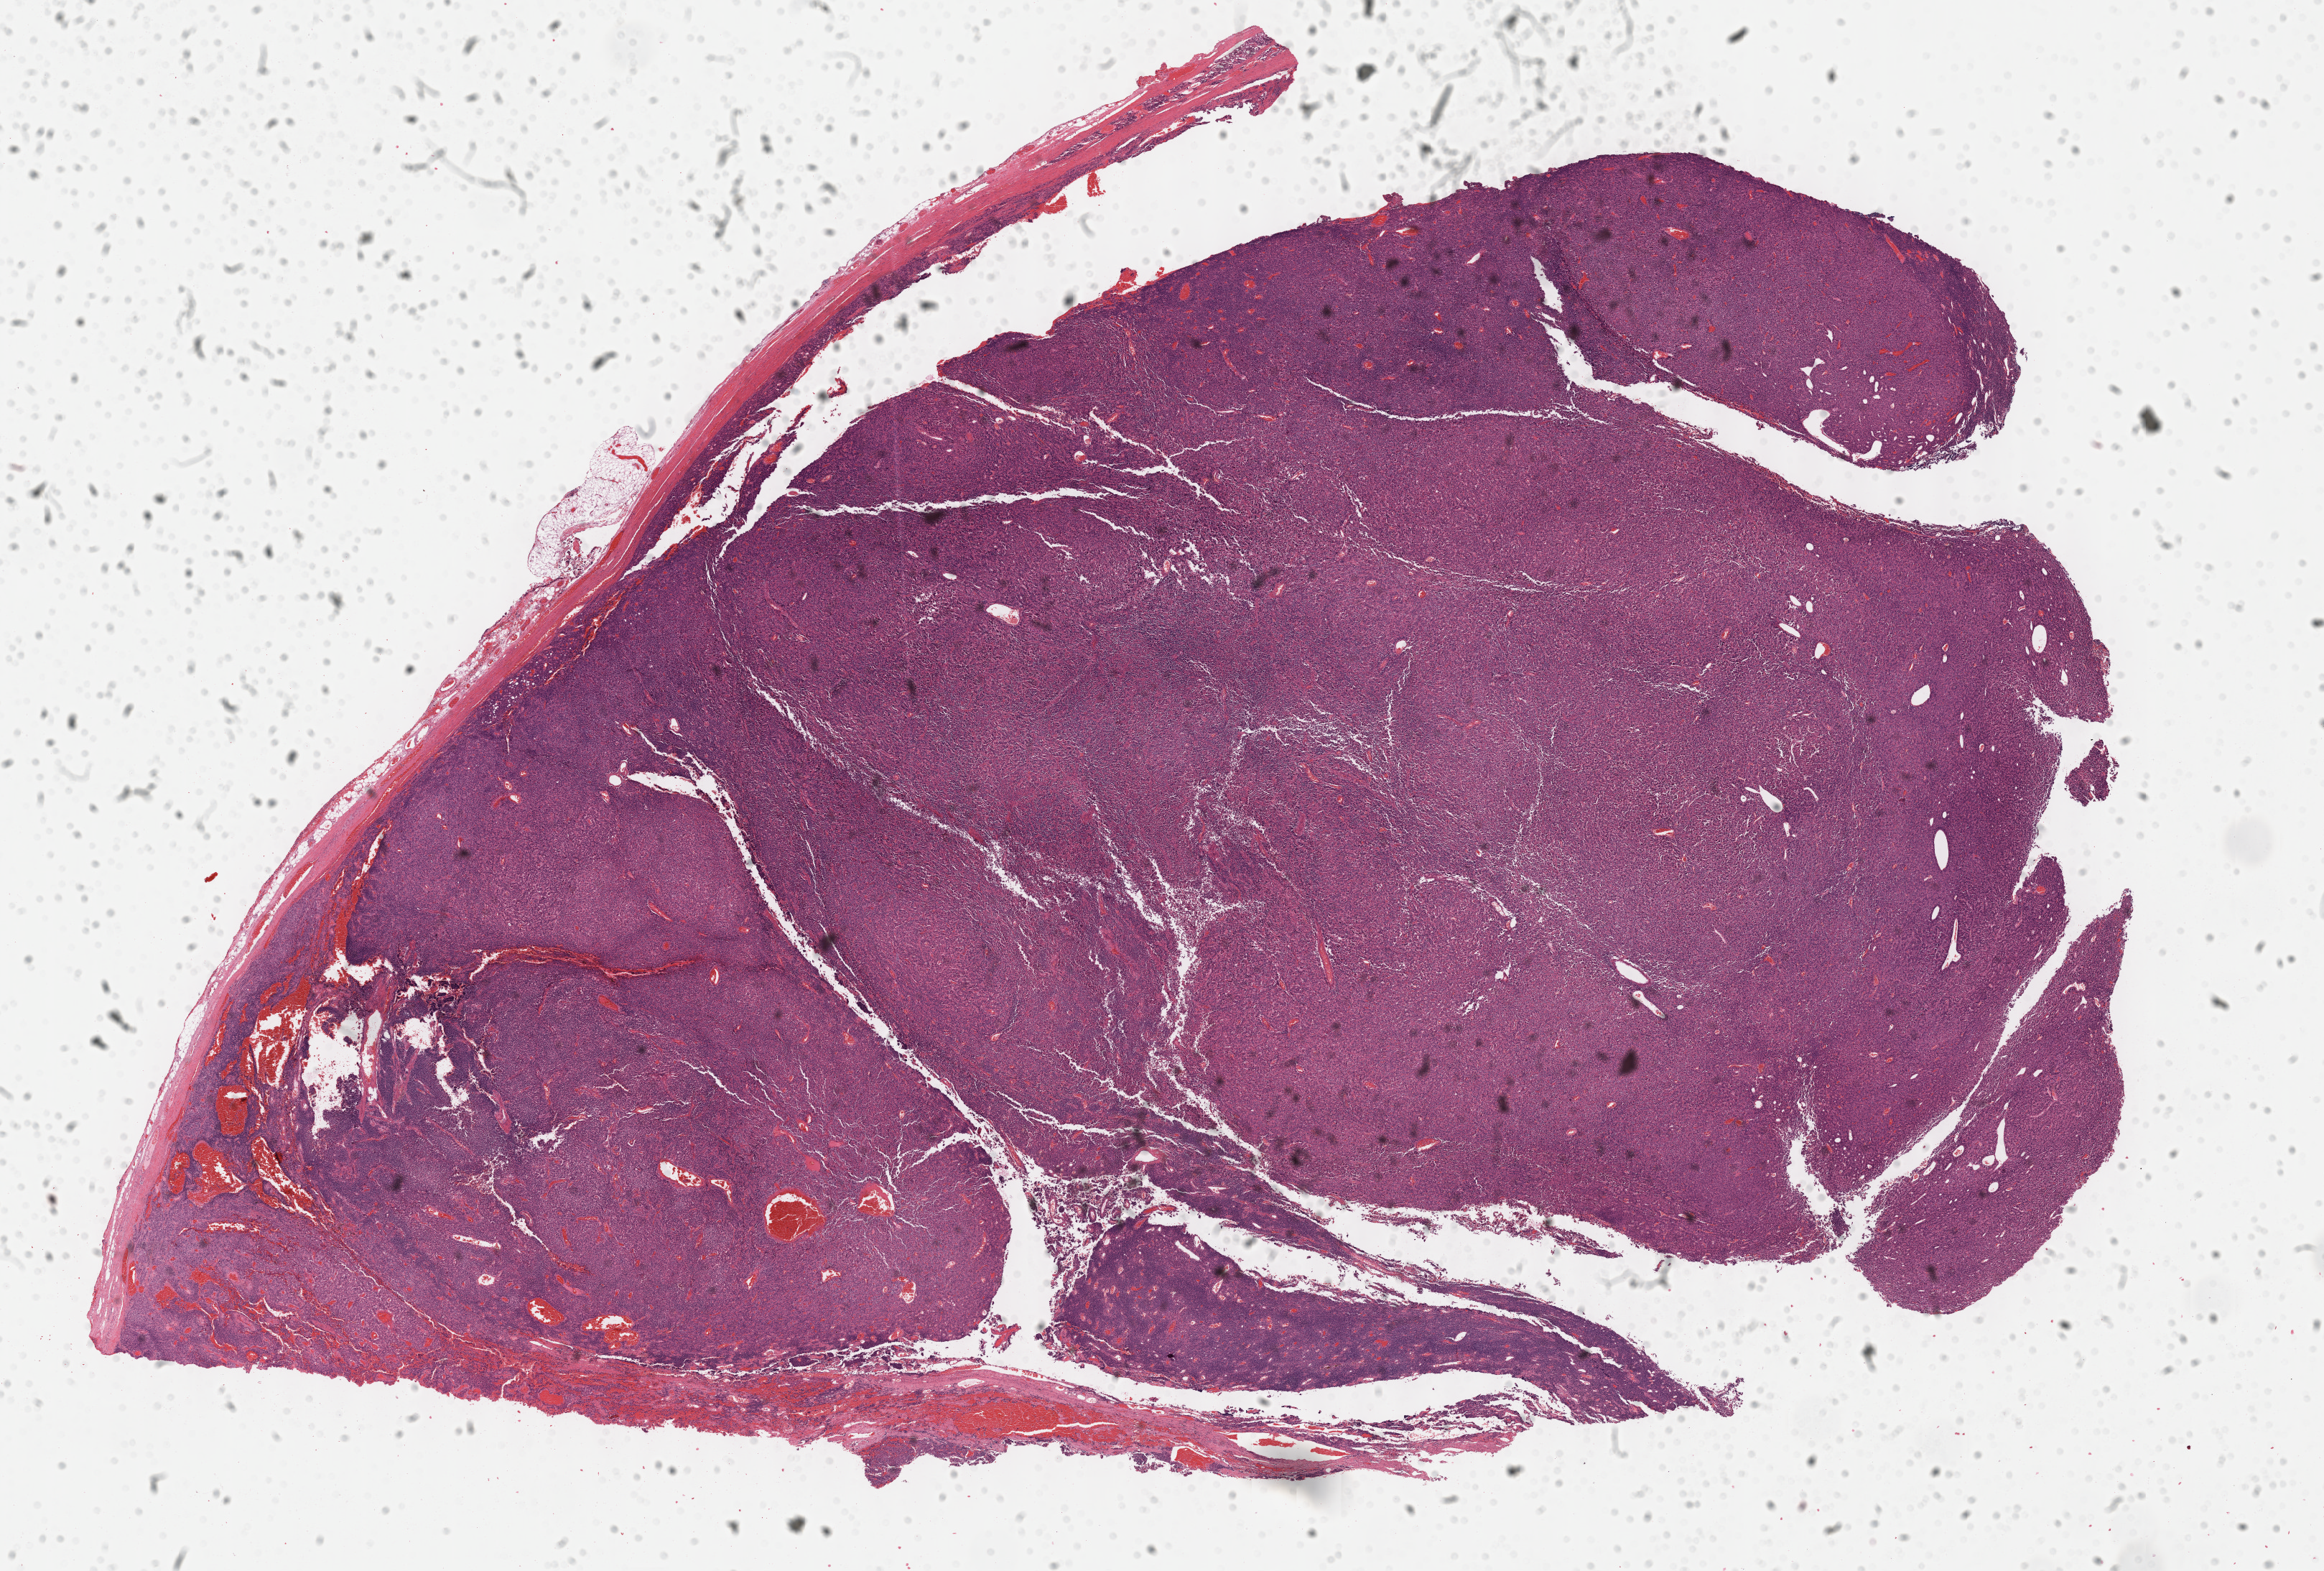
H&E whole-slide image — low-resolution overview of the scanned area, about 26.2 x 17.7 mm (from a 40x scan), FFPE section, sample: primary tumour, adrenal cortex. Male patient; age at initial diagnosis 58 years.
• laterality: left
• diagnosis: Adrenal cortical carcinoma (cortex of adrenal gland)